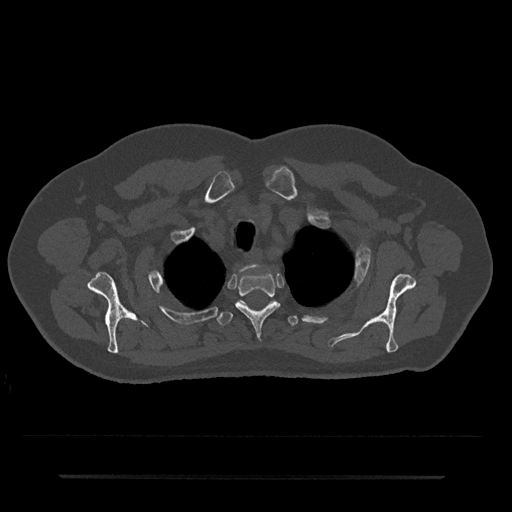
CT including the spine, one axial slice. Slice 598 of 797 in the series (ordered by position). 120 kVp. Bone window (W 1800 / L 400 HU). 512 × 512 image matrix, field of view 437 × 437 mm. Male patient, age 69 years. Case-level facts recorded for this patient, not image findings: primary cancer: prostate.
Outlined on this slice (semi-automatically segmented with operator editing):
- T1 vertebra: bounding box (x1, y1, x2, y2) in pixels: (242, 265, 256, 271)
- T2 vertebra: (235, 272, 280, 336)
- T3 vertebra: (217, 300, 298, 326)